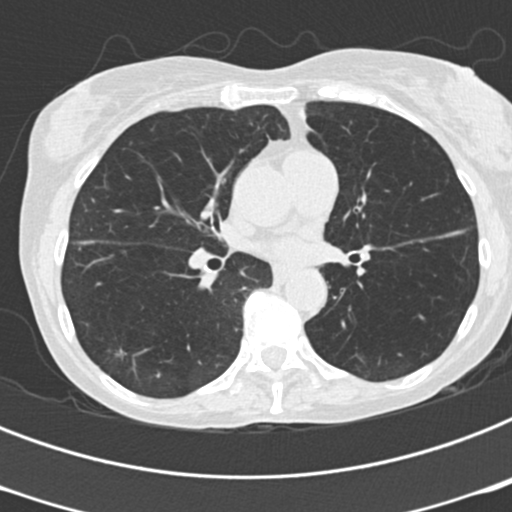
Low-dose screening chest CT, one axial slice. Position 110 of 199 along the scan axis. Reconstruction kernel B30f. 120 kVp. Lung window (W 1500 / L -600 HU). 2 mm slice thickness. 512 × 512 image matrix.
Structures marked on this image (outlined manually by an expert reader):
- lesion 1 (tumor, lower lobe of right lung): bounding box (x1, y1, x2, y2) in pixels: (115, 348, 127, 358)